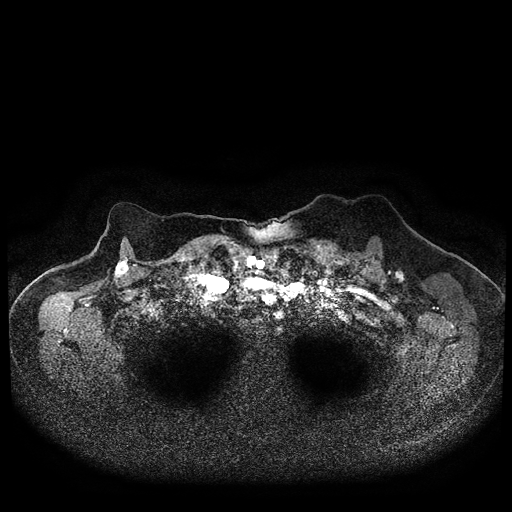
Breast MRI (dynamic contrast-enhanced, multi-phase), one axial slice; slice 83 of 116 in the series (ordered by position); dynamic contrast-enhanced series, time point 2 of 5 at this slice position (early post-contrast); 1.5 T; TE 2.7 ms, TR 5.4 ms; 2 mm slice thickness; 512 × 512 image matrix. Female patient, age 72 years.
Annotated regions visible in this slice (semi-automatic segmentation, software-assisted and operator-edited):
- breast lesion (labelled 'tumour' in the annotation; benign lesions carry a separate 'benign' label): bounding box (x1, y1, x2, y2) in pixels: (114, 254, 131, 280)